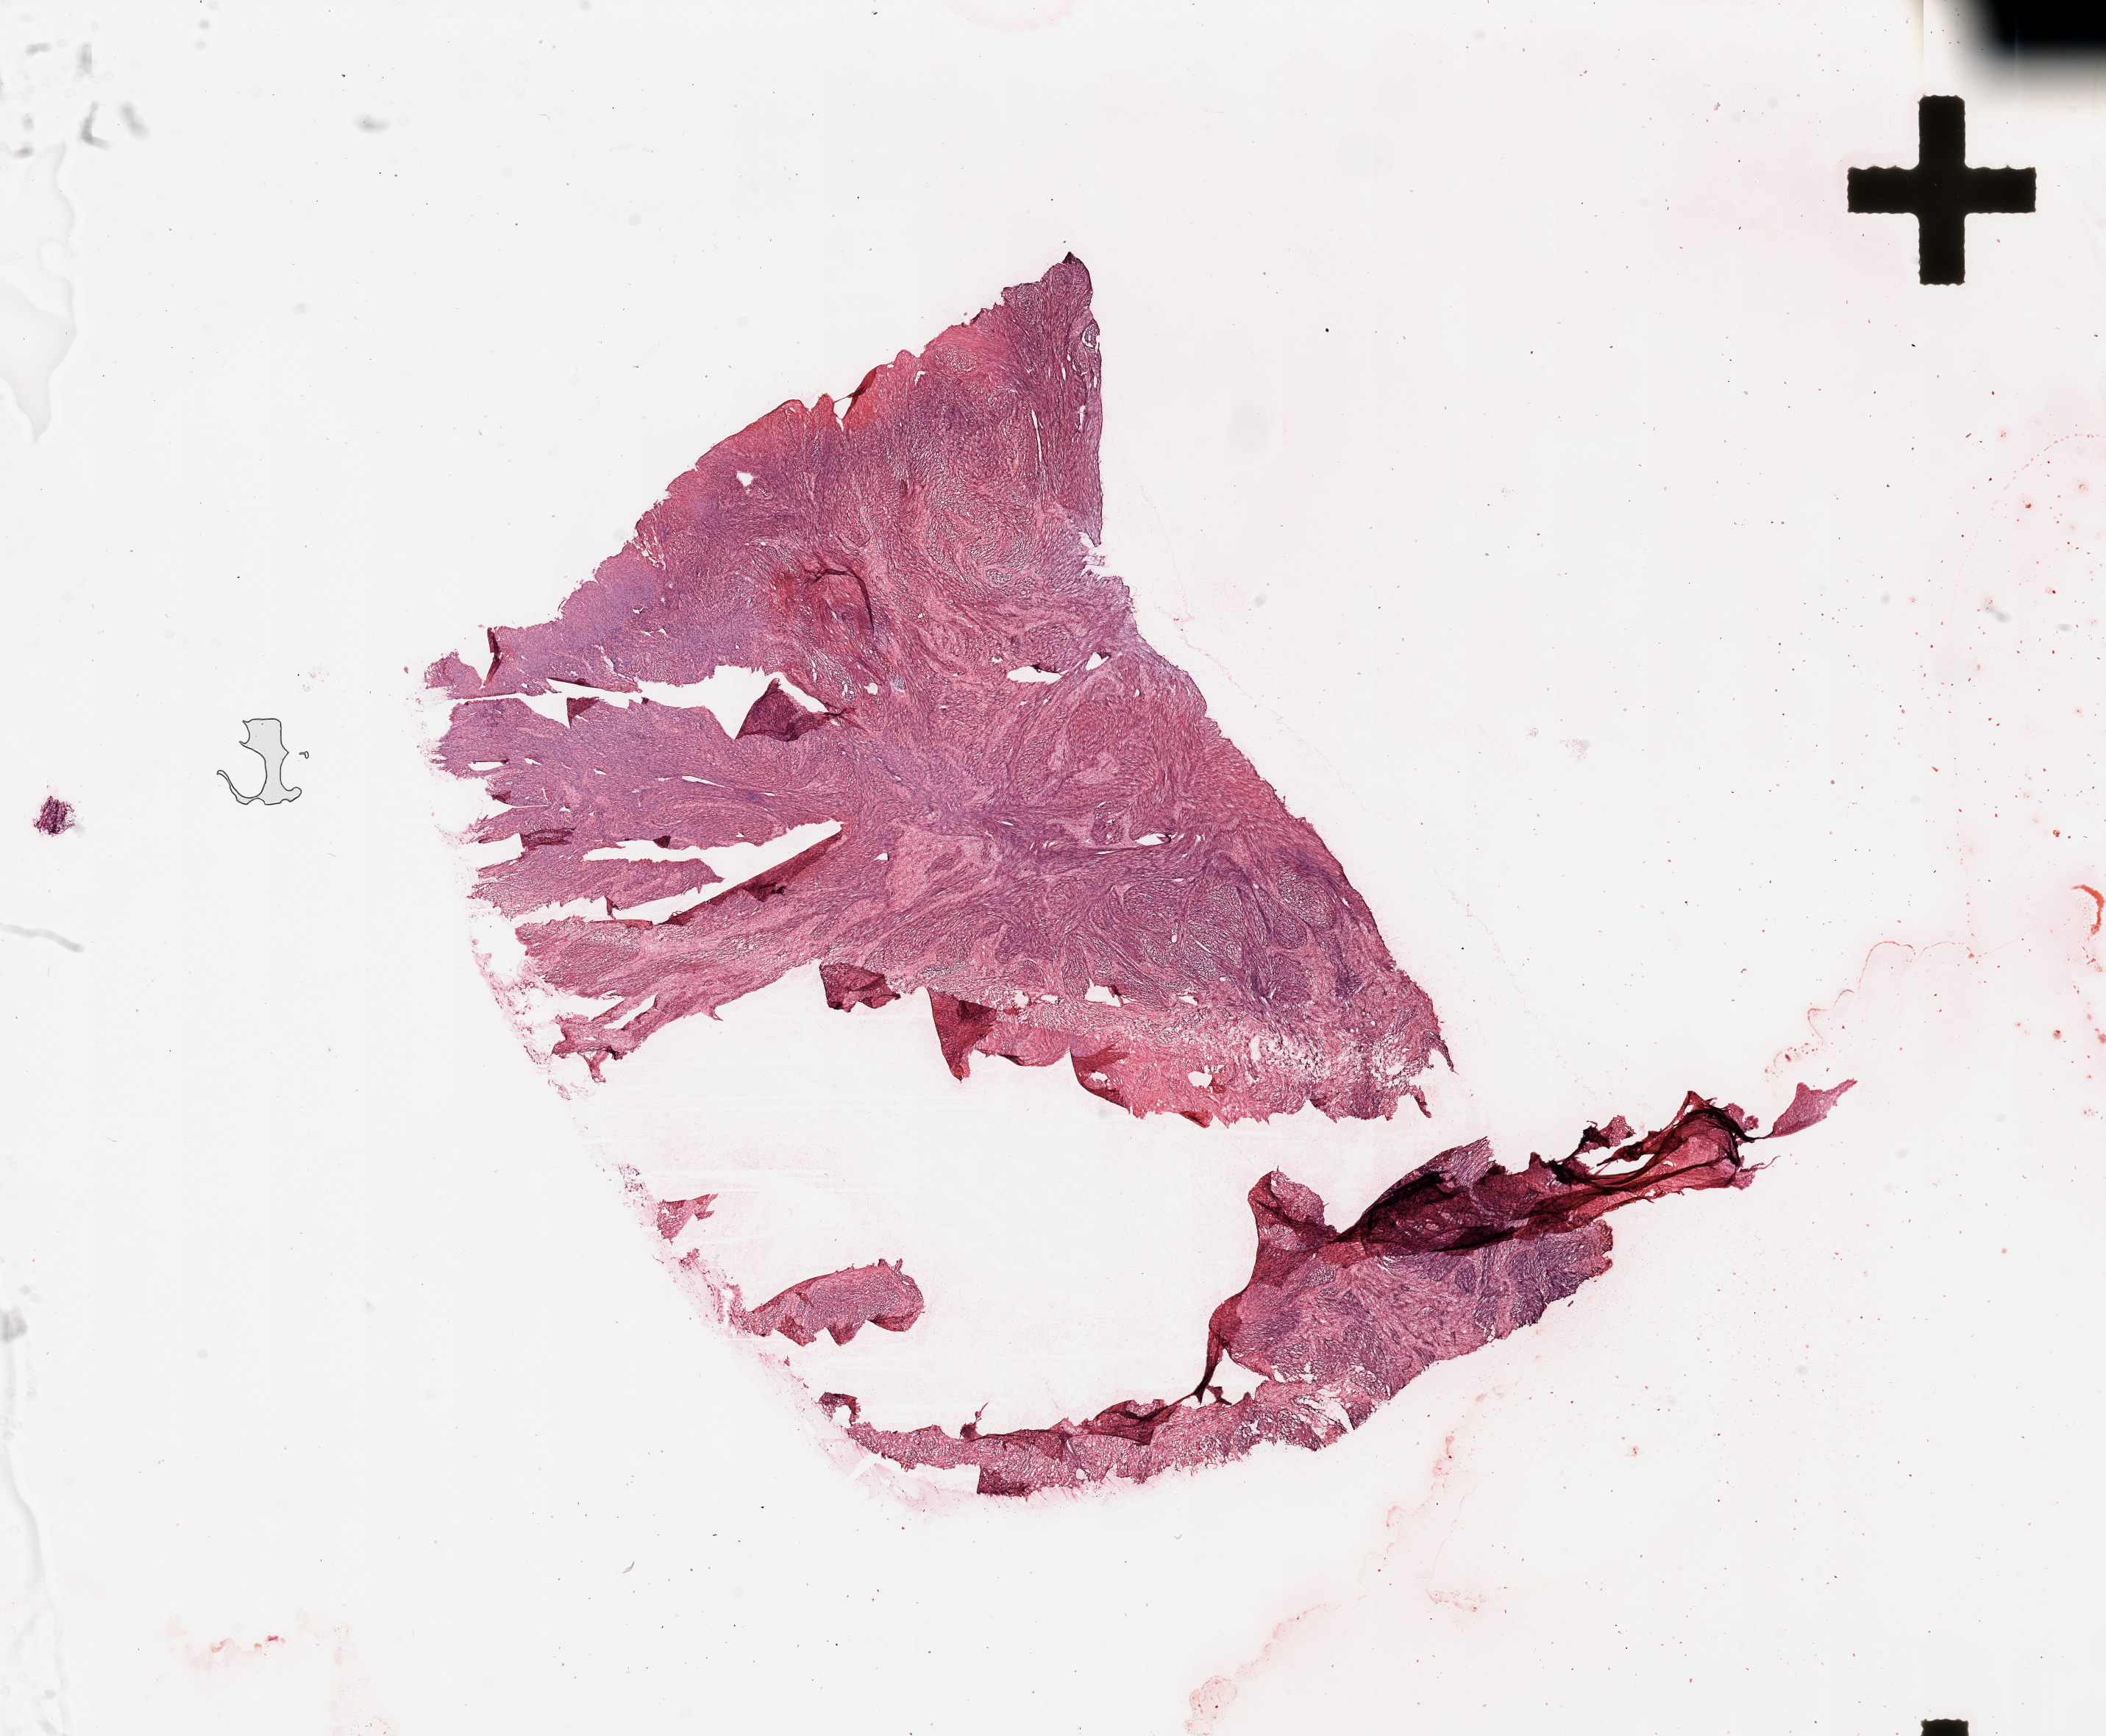
Hematoxylin and eosin (H&E) stained whole-slide image — low-resolution overview of the scanned area, about 22.6 x 18.7 mm (from a 20x scan). Tumour tissue sample. 42-year-old female patient.
Patient diagnosis (cohort enrolment): sarcoma (site not recorded at cohort level). Primary tumour site (as recorded): chest.